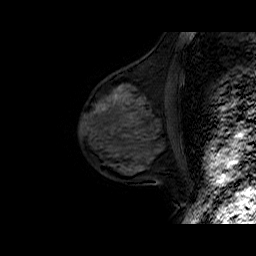
Breast MRI (dynamic contrast-enhanced), one sagittal slice. Position 25 of 50 along the scan axis. Dynamic contrast-enhanced series, time point 2 of 6 at this slice position (early post-contrast). 1.5 T. TE 6.5 ms, TR 32.9 ms. 256 × 256 image matrix. Female patient. Case-level facts recorded for this patient, not image findings: setting: breast cancer imaged before/during neoadjuvant chemotherapy; receptor status: HR-positive, HER2-negative.
Annotated regions visible in this slice (semi-automatically segmented with operator editing):
- analysis volume of interest (the breast-tissue region the enhancement analysis was run in; not a lesion): bounding box (x1, y1, x2, y2) in pixels: (79, 75, 179, 149)
- tumour enhancement mask (voxels above the 100 % enhancement threshold inside the analysis volume of interest): (102, 109, 104, 111)